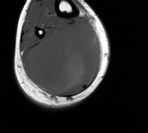
MRI of an extremity soft-tissue mass, one axial slice; slice 46 of 76 in the series (ordered by position); MR volume resampled by the dataset authors to the PET/CT grid (not the native acquisition matrix); 3.27 mm slice thickness; 148 × 133 image matrix, field of view 145 × 130 mm. Male patient. Case-level facts recorded for this patient, not image findings: histological type: liposarcoma - round cell; grade: high; site of the primary tumour: right calf.
Structures marked on this image (expert contour drawn on MRI and transferred to this co-registered scan by the dataset authors):
- gross tumour volume (mass): bounding box (x1, y1, x2, y2) in pixels: (26, 23, 101, 93)